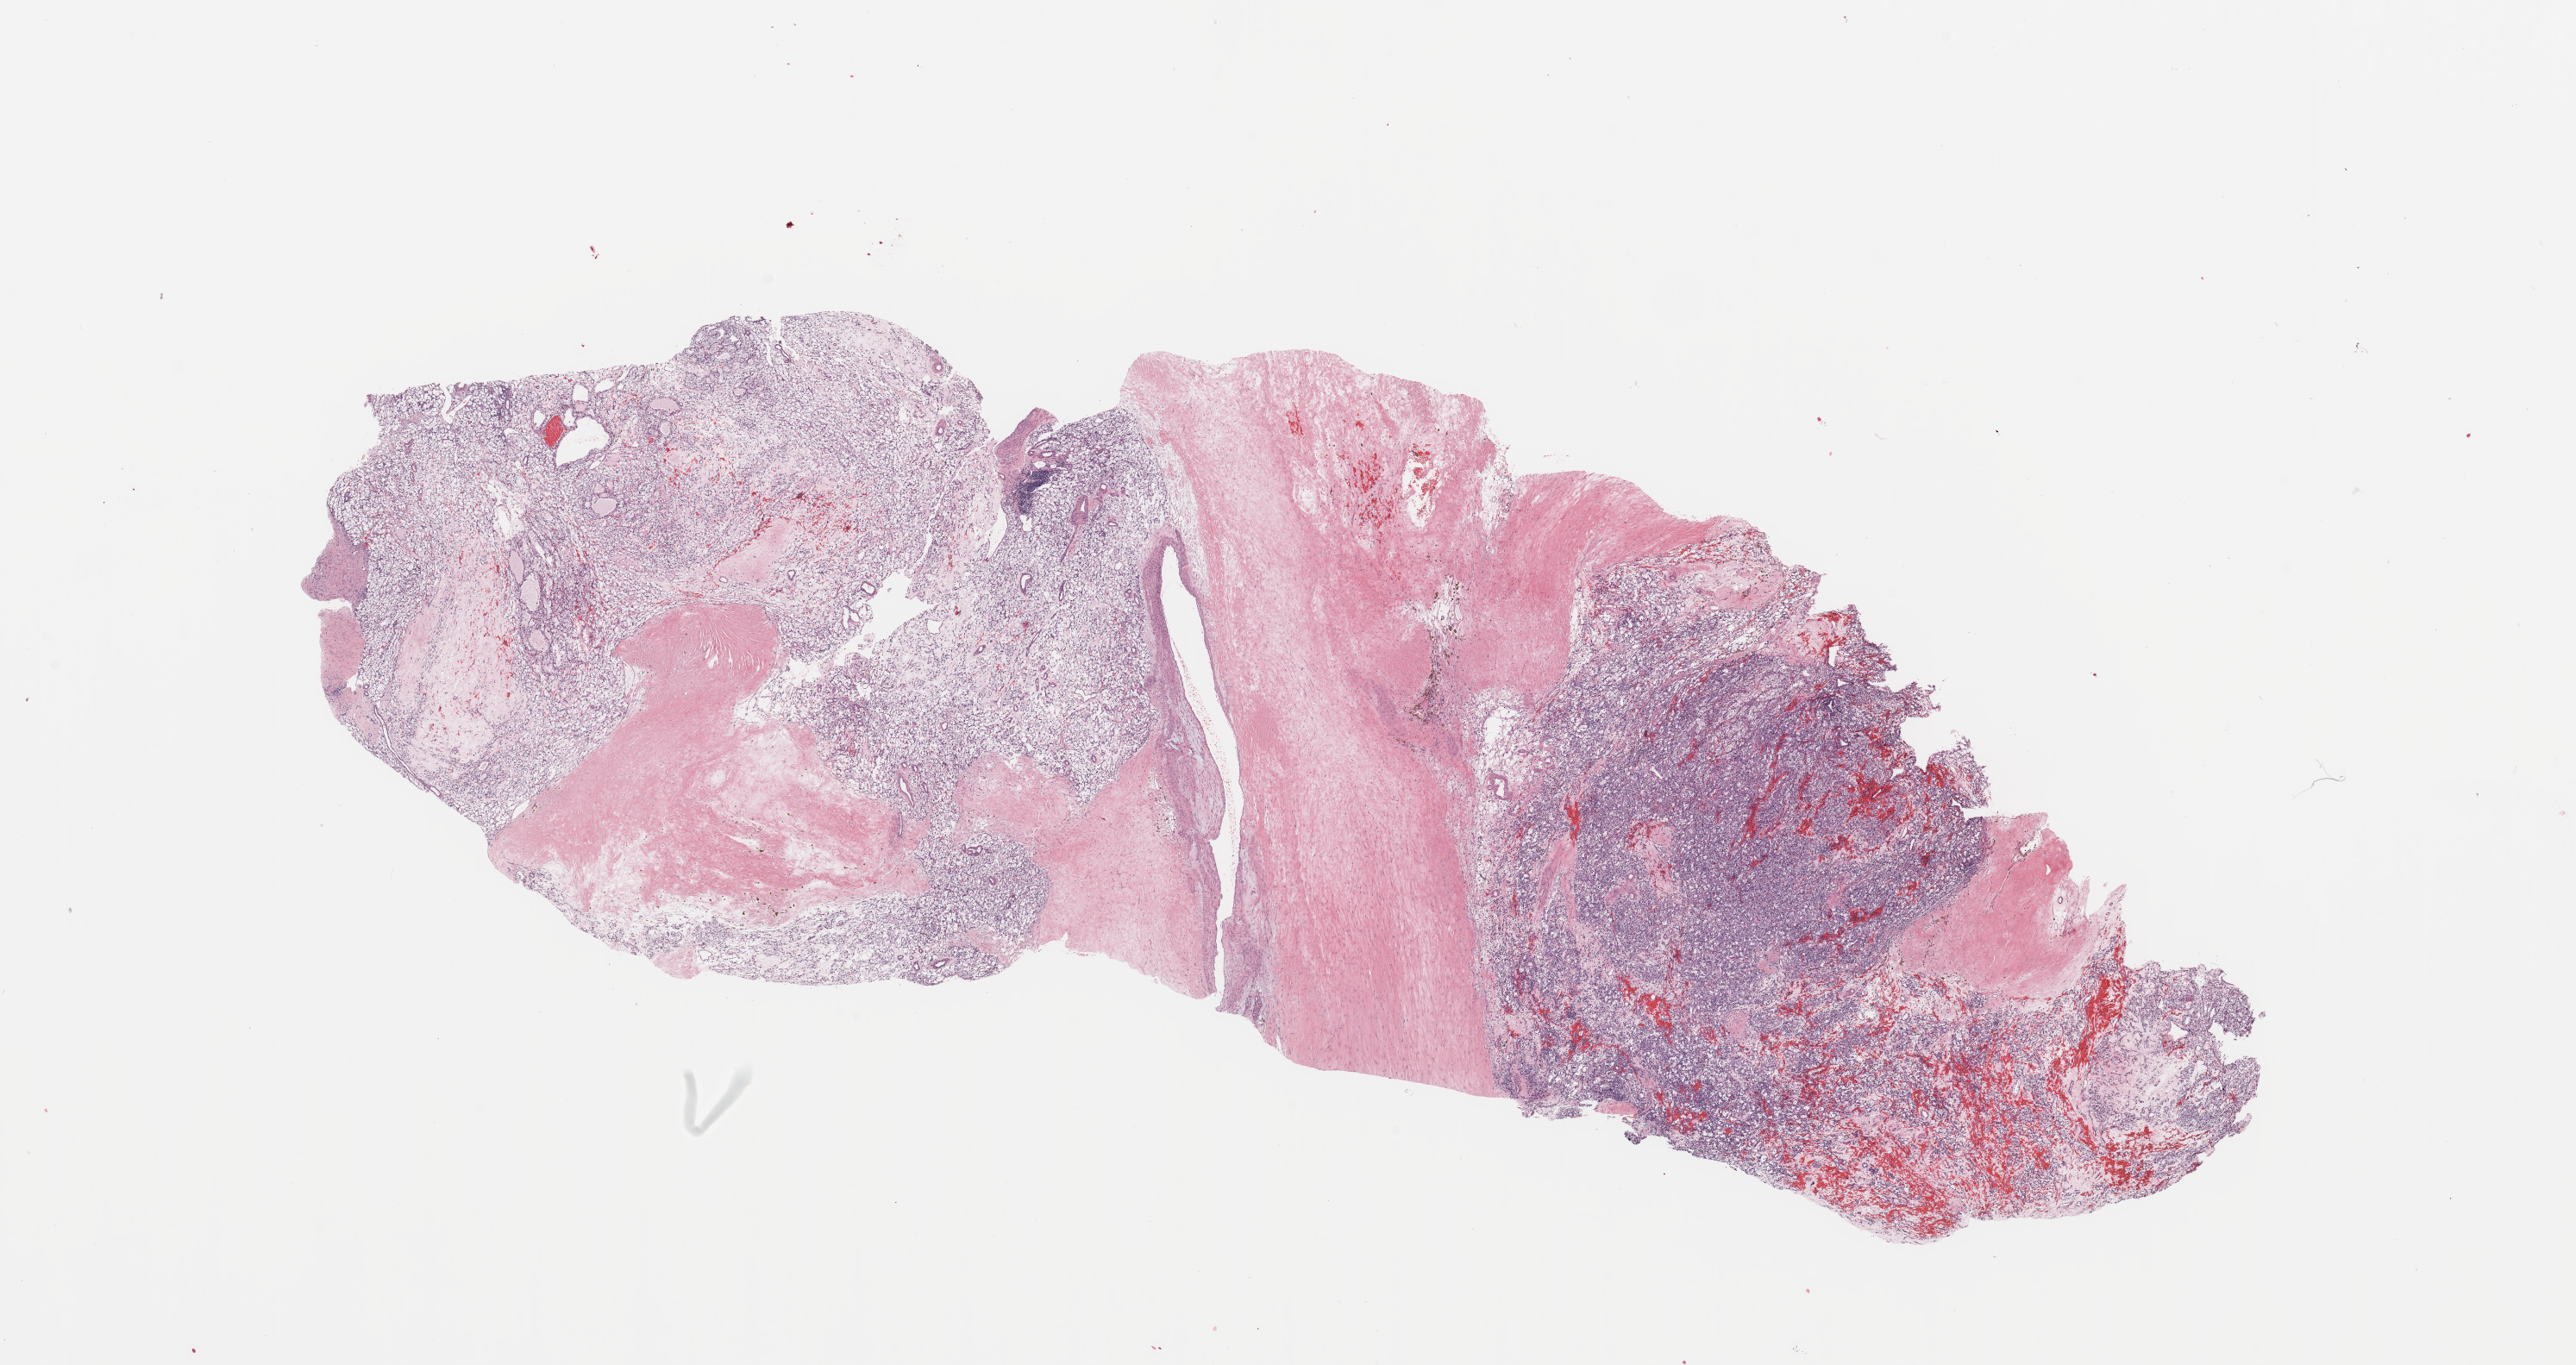
Digitized Hematoxylin and eosin (H&E) stained tissue section (whole slide) — low-resolution overview of the scanned area, about 23.6 x 12.5 mm (acquisition: 20x scan). Tumour tissue sample, sampled site: kidney. Patient: male, age 33 years. Histologic grade: G2 (moderately differentiated). Pathologist review of this section (percent, as recorded): tumour nuclei 80%, necrosis 5%.
Diagnosis: Renal cell carcinoma, NOS. Primary tumour site (as recorded): upper pole. AJCC pathologic stage: I.